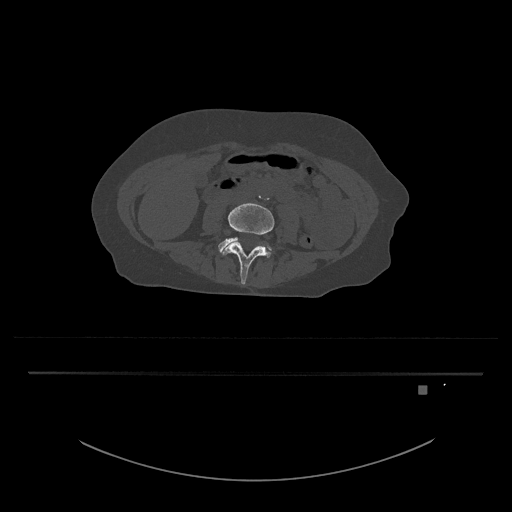
CT including the spine, one axial slice. Position 351 of 797 along the scan axis. Reconstruction kernel Br40s/3. Bone window (W 1800 / L 400 HU). 512 × 512 image matrix, field of view 500 × 500 mm. Female patient, age 57 years. Case-level facts recorded for this patient, not image findings: primary cancer: cervical.
Outlined on this slice (semi-automatically segmented with operator editing):
- L4 vertebra: bounding box [x1, y1, x2, y2] px = [220, 203, 275, 285]